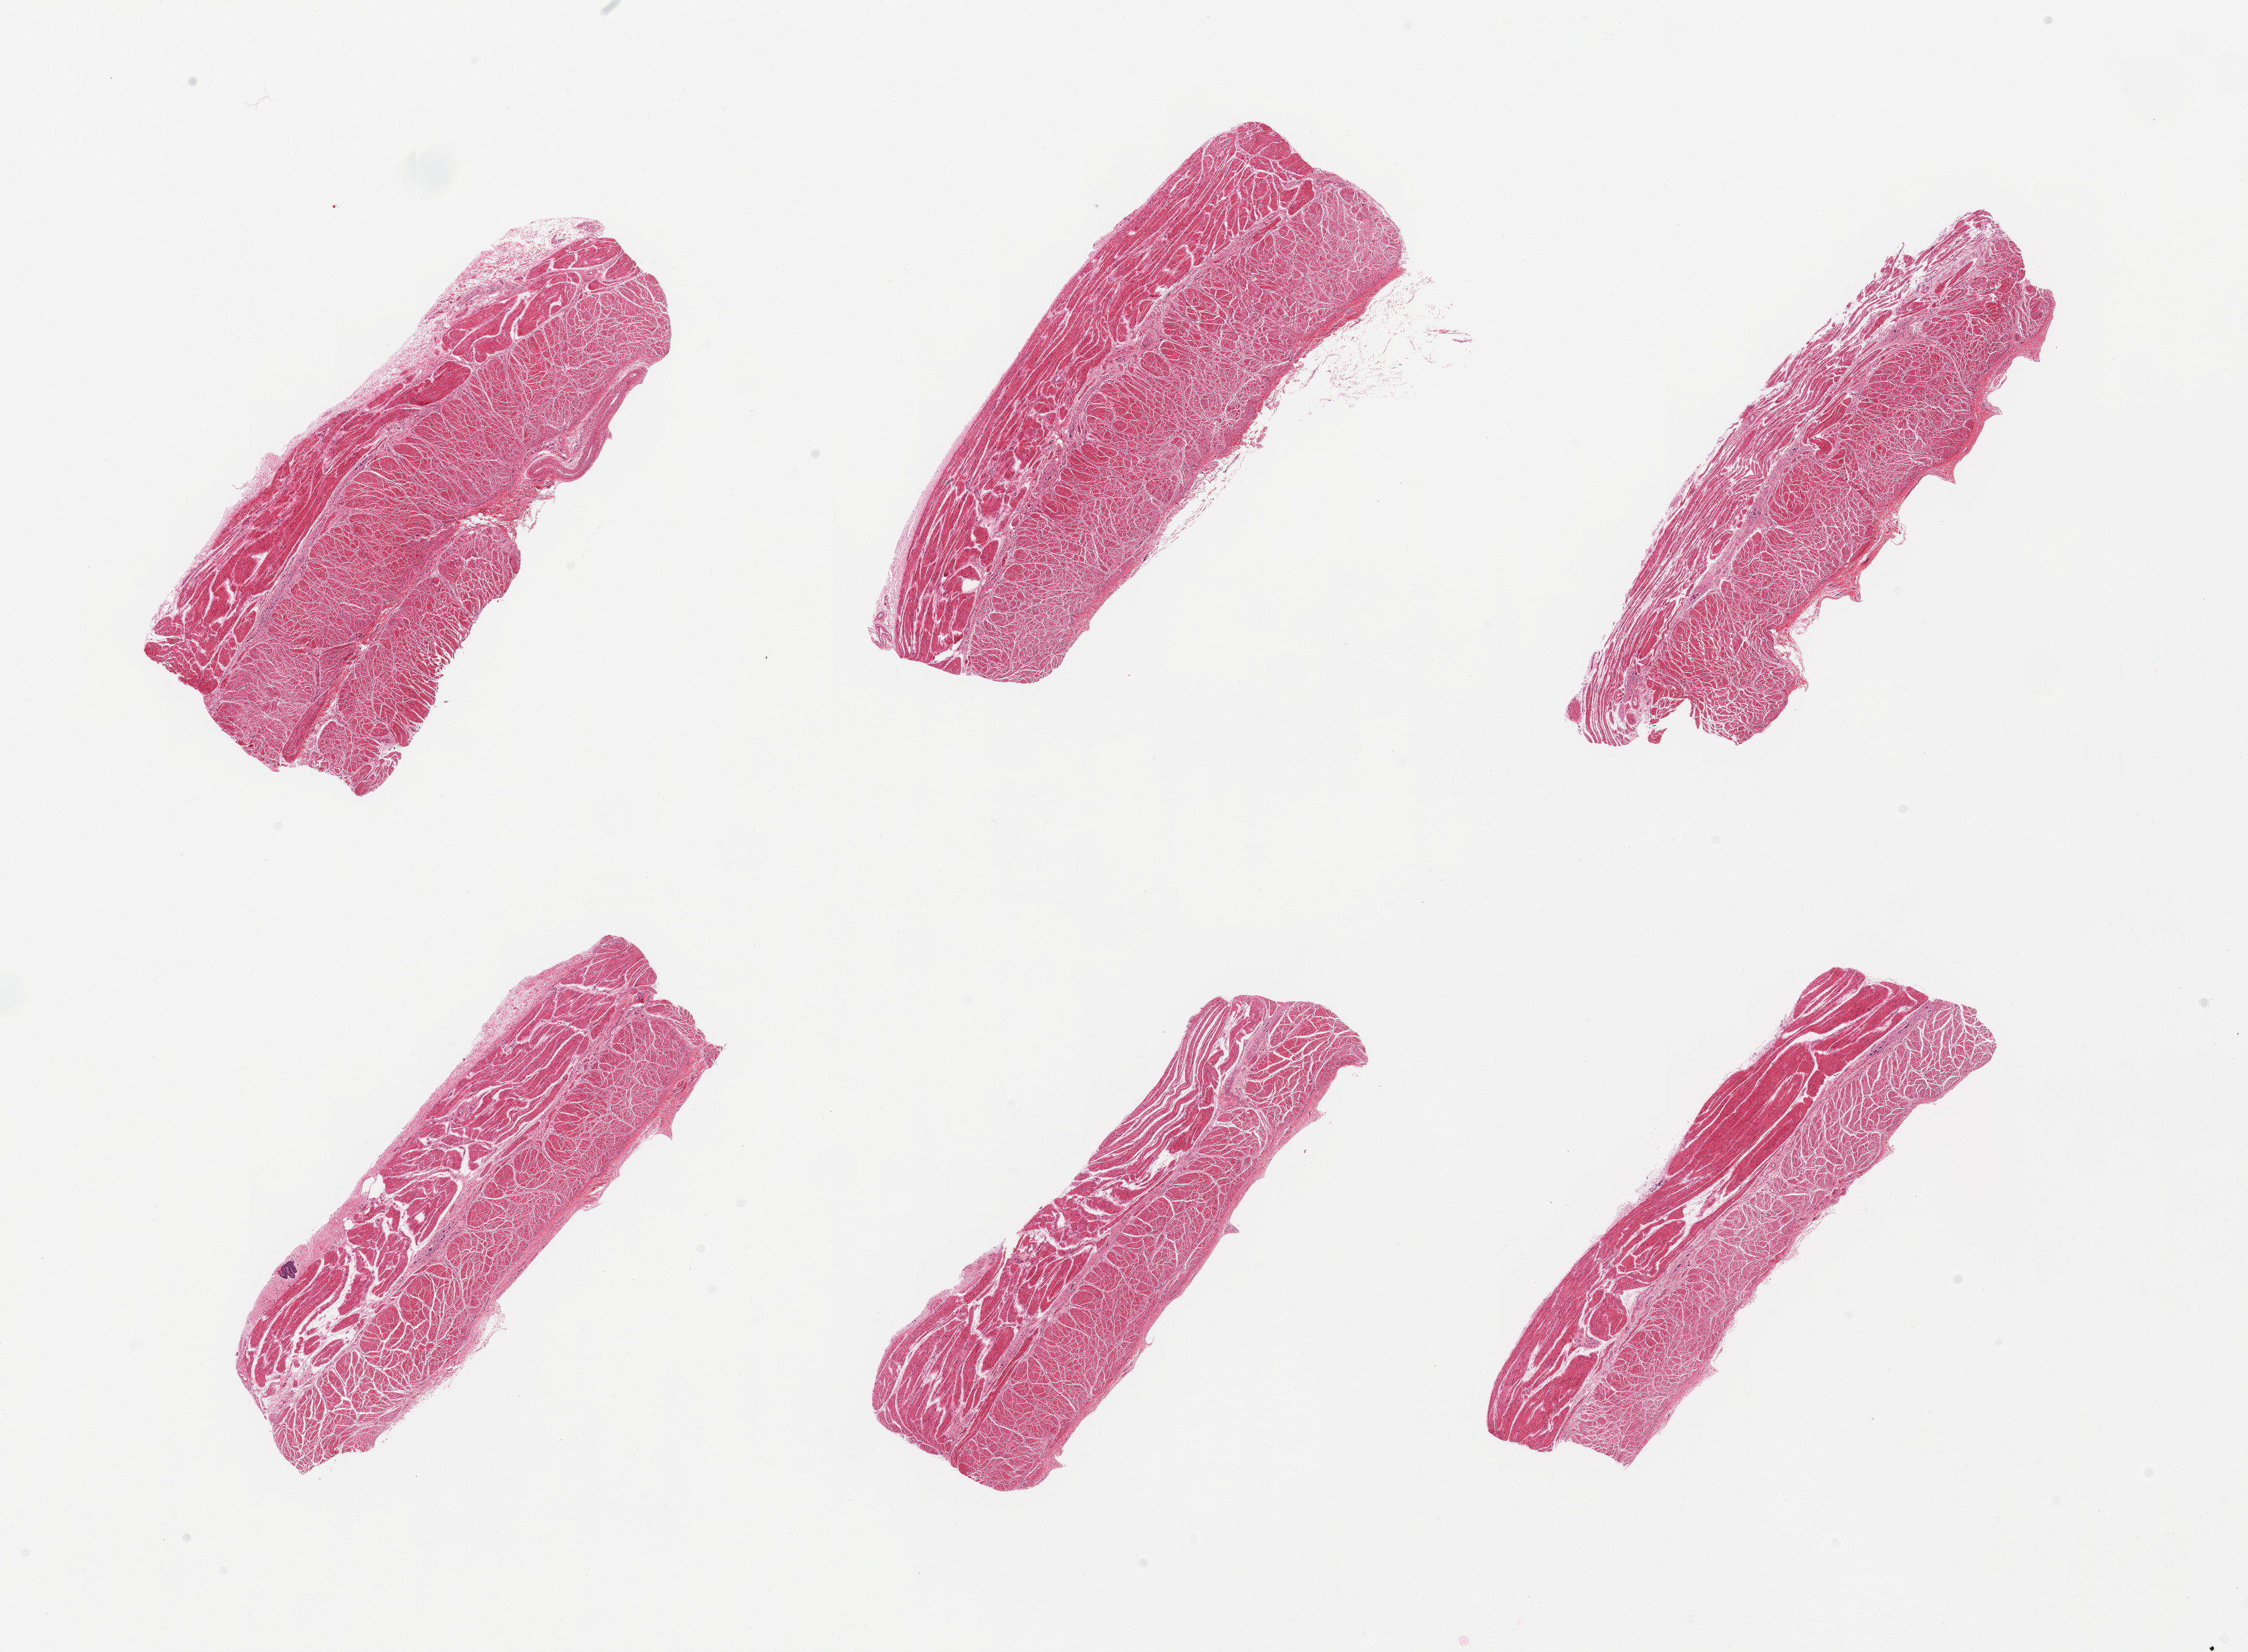
Hematoxylin and eosin (H&E) whole-slide image, shown as a low-resolution overview of the whole scanned area (about 26.6 x 19.5 mm). PAXgene-fixed, paraffin-embedded tissue. Sampled site (target tissue): esophageal muscle. Tissue donor sample. Donor: female.
* pathologist's review note for this sample: 6 pieces; well trimmed, small detached fragment of squamous epithelium